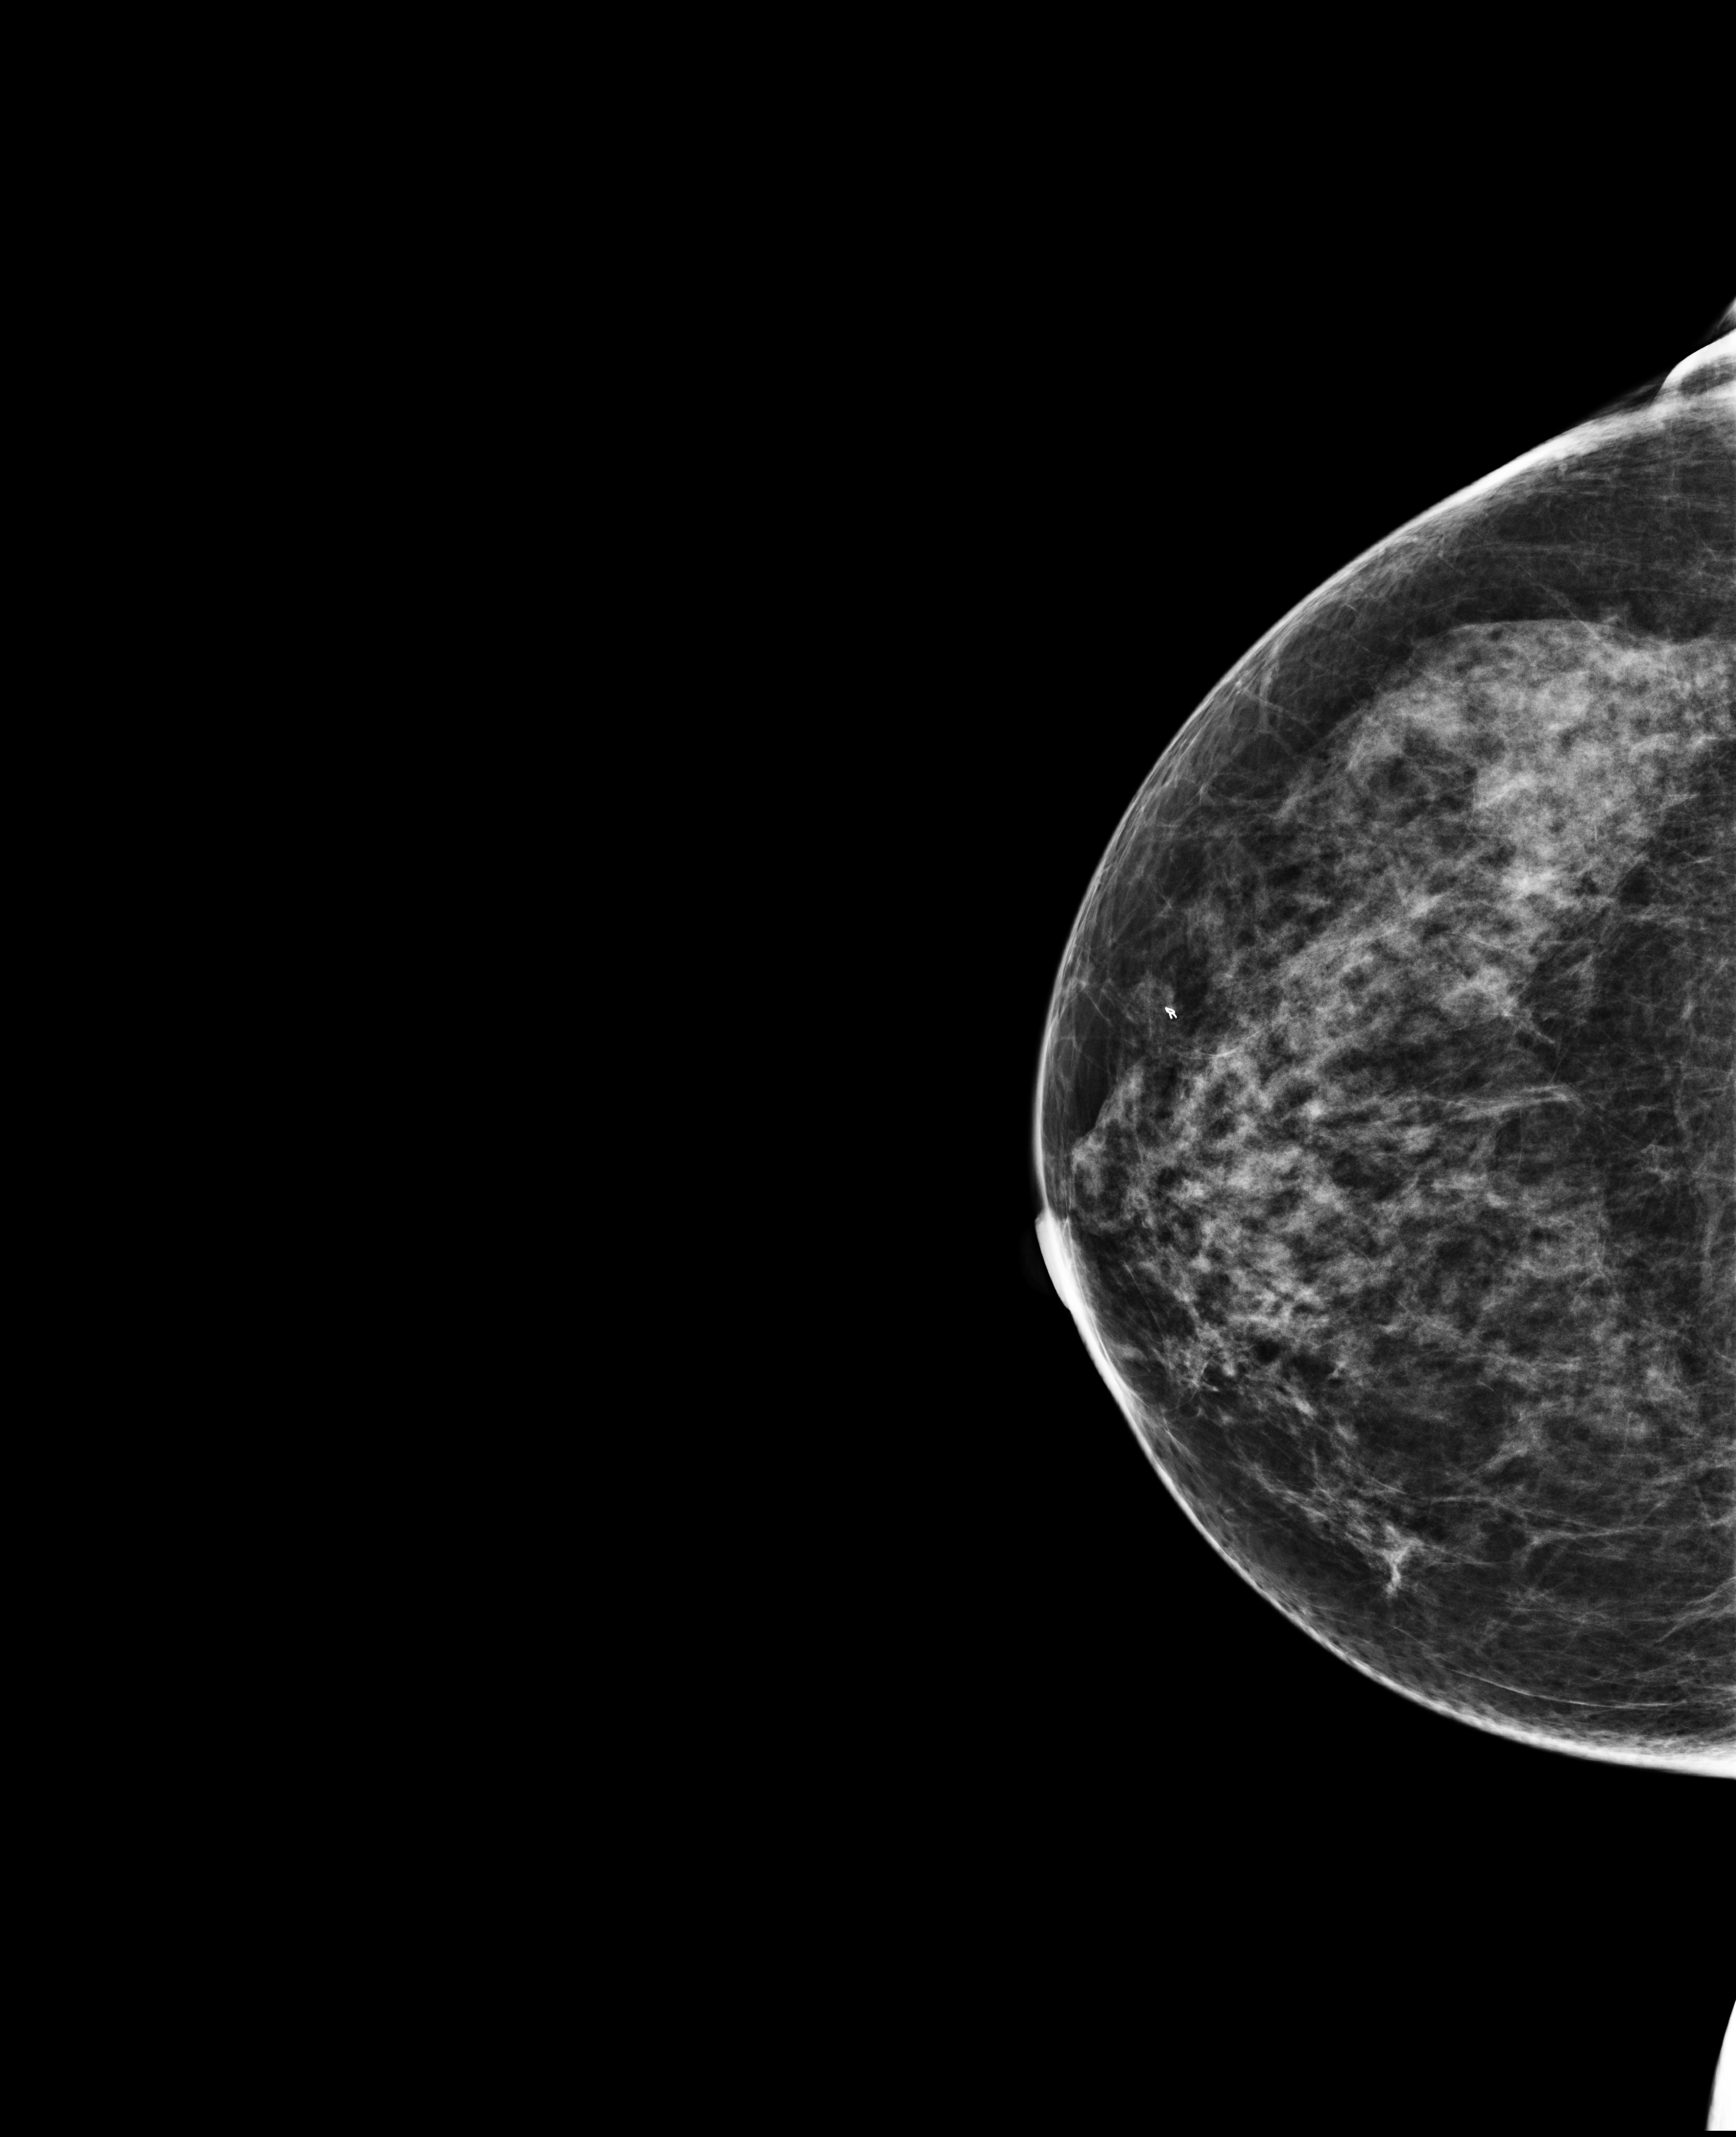
Screening examination.
Image type: full-field digital mammogram. Breast: right. Projection: cranio-caudal projection.